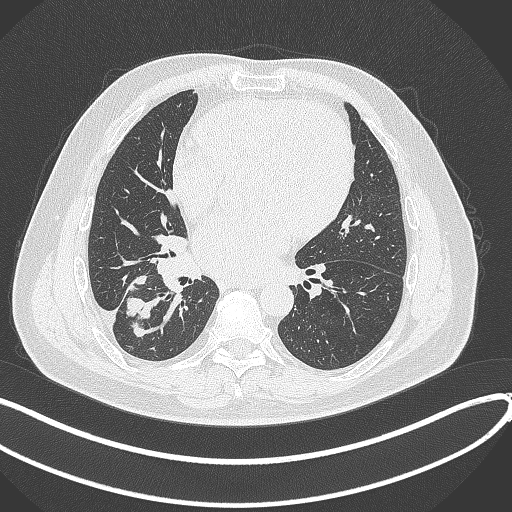
Chest CT, one axial slice; slice 166 of 360 in the series (ordered by position); reconstruction kernel B70f; 120 kVp; lung window (W 1500 / L -600 HU); 512 × 512 image matrix, field of view 400 × 400 mm. Male patient, age 59 years.
Annotated regions visible in this slice (bounding box drawn by a radiologist):
- lung tumour (recorded histology: adenocarcinoma): box from (x=125, y=272) to (x=160, y=338) px